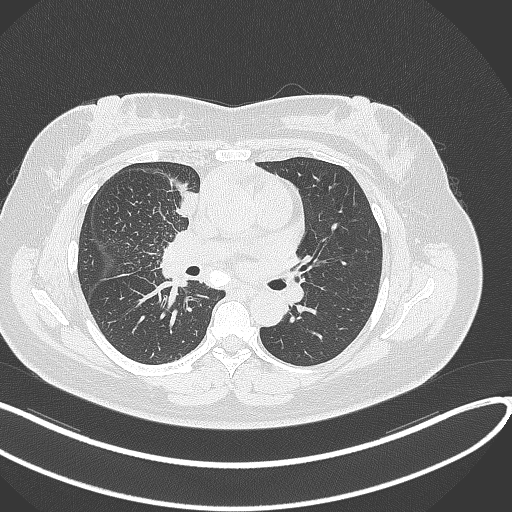
Chest CT, one axial slice. Position 145 of 303 along the scan axis. Reconstruction kernel B70f. 120 kVp. Lung window (W 1500 / L -600 HU). 1 mm slice thickness. 512 × 512 image matrix, field of view 400 × 400 mm. Patient: female, 46 years. Case-level facts recorded for this patient, not image findings: clinical TNM (as recorded): T2a N1 M0.
Annotated regions visible in this slice (bounding box drawn by a radiologist):
- lung tumour (recorded histology: adenocarcinoma): bounding box (x1, y1, x2, y2) in pixels: (175, 190, 201, 221)